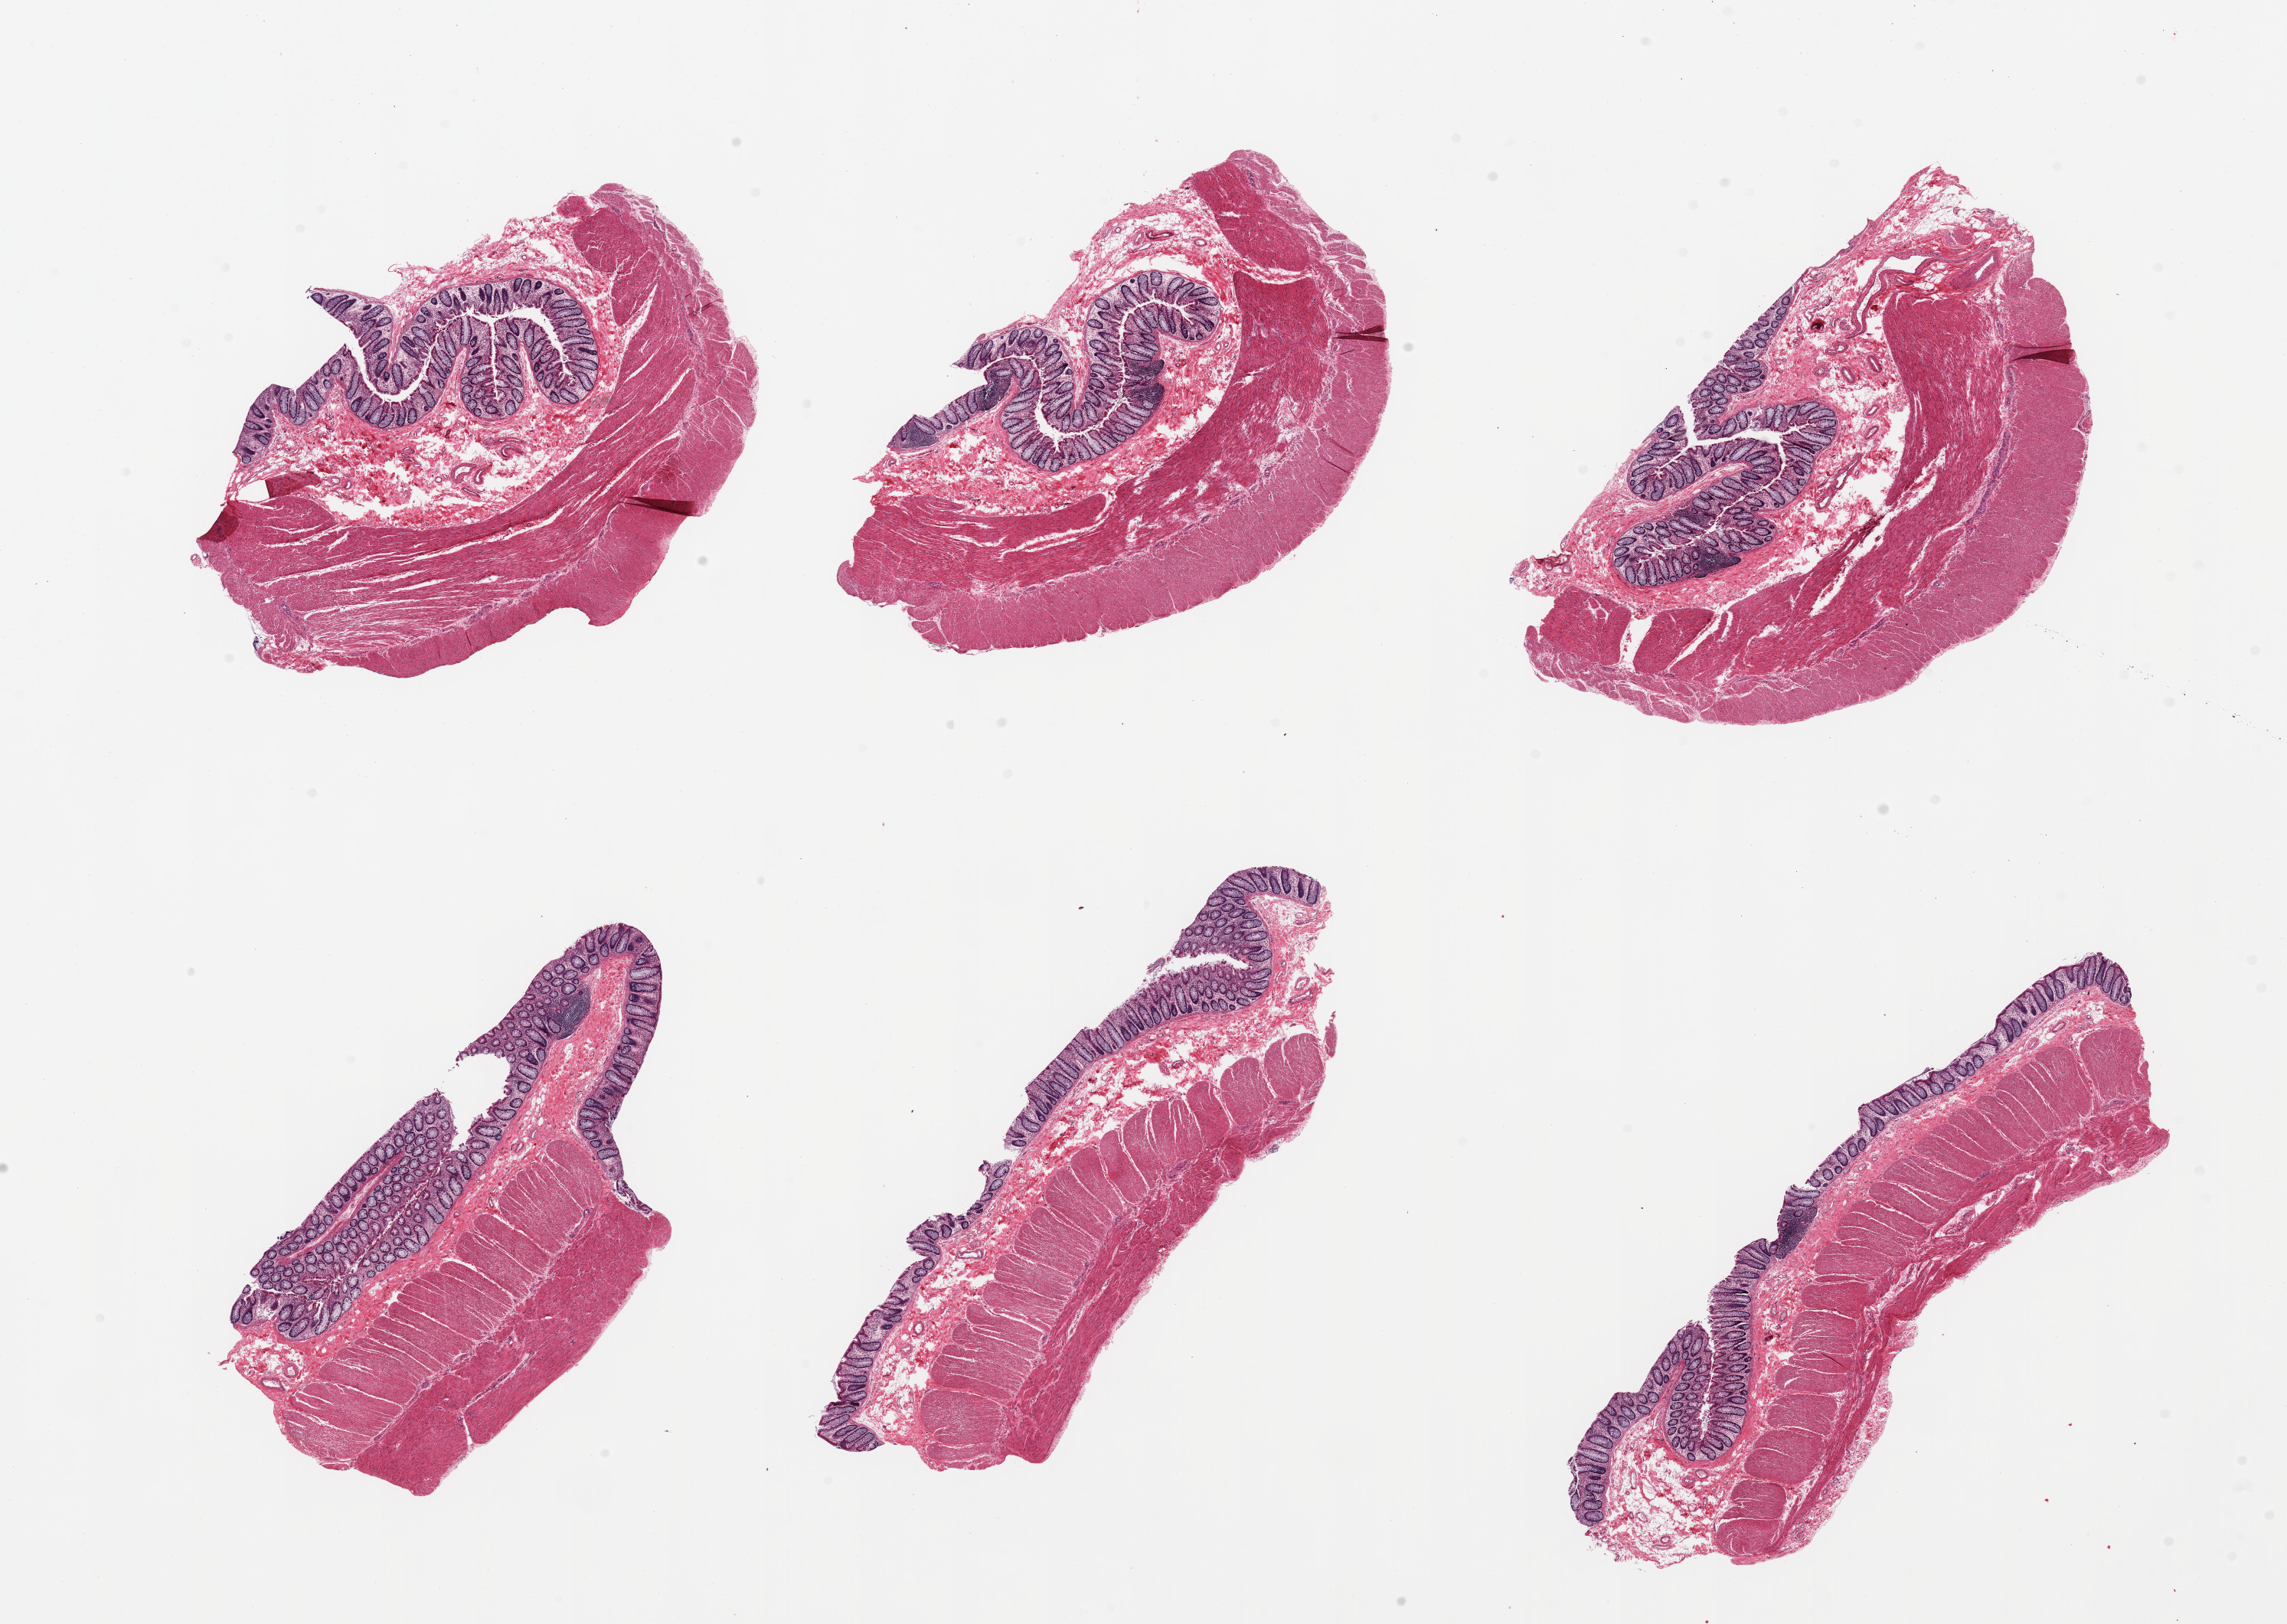
Digitized H&E-stained section, whole scanned area (about 23.6 x 16.8 mm) shown as a low-resolution overview, PAXgene-fixed, paraffin-embedded tissue, target tissue: transverse colon, donor tissue sample. Donor: female.
Review note (as recorded): 6 pieces; well preserved colonic target mucosa and muscularis.